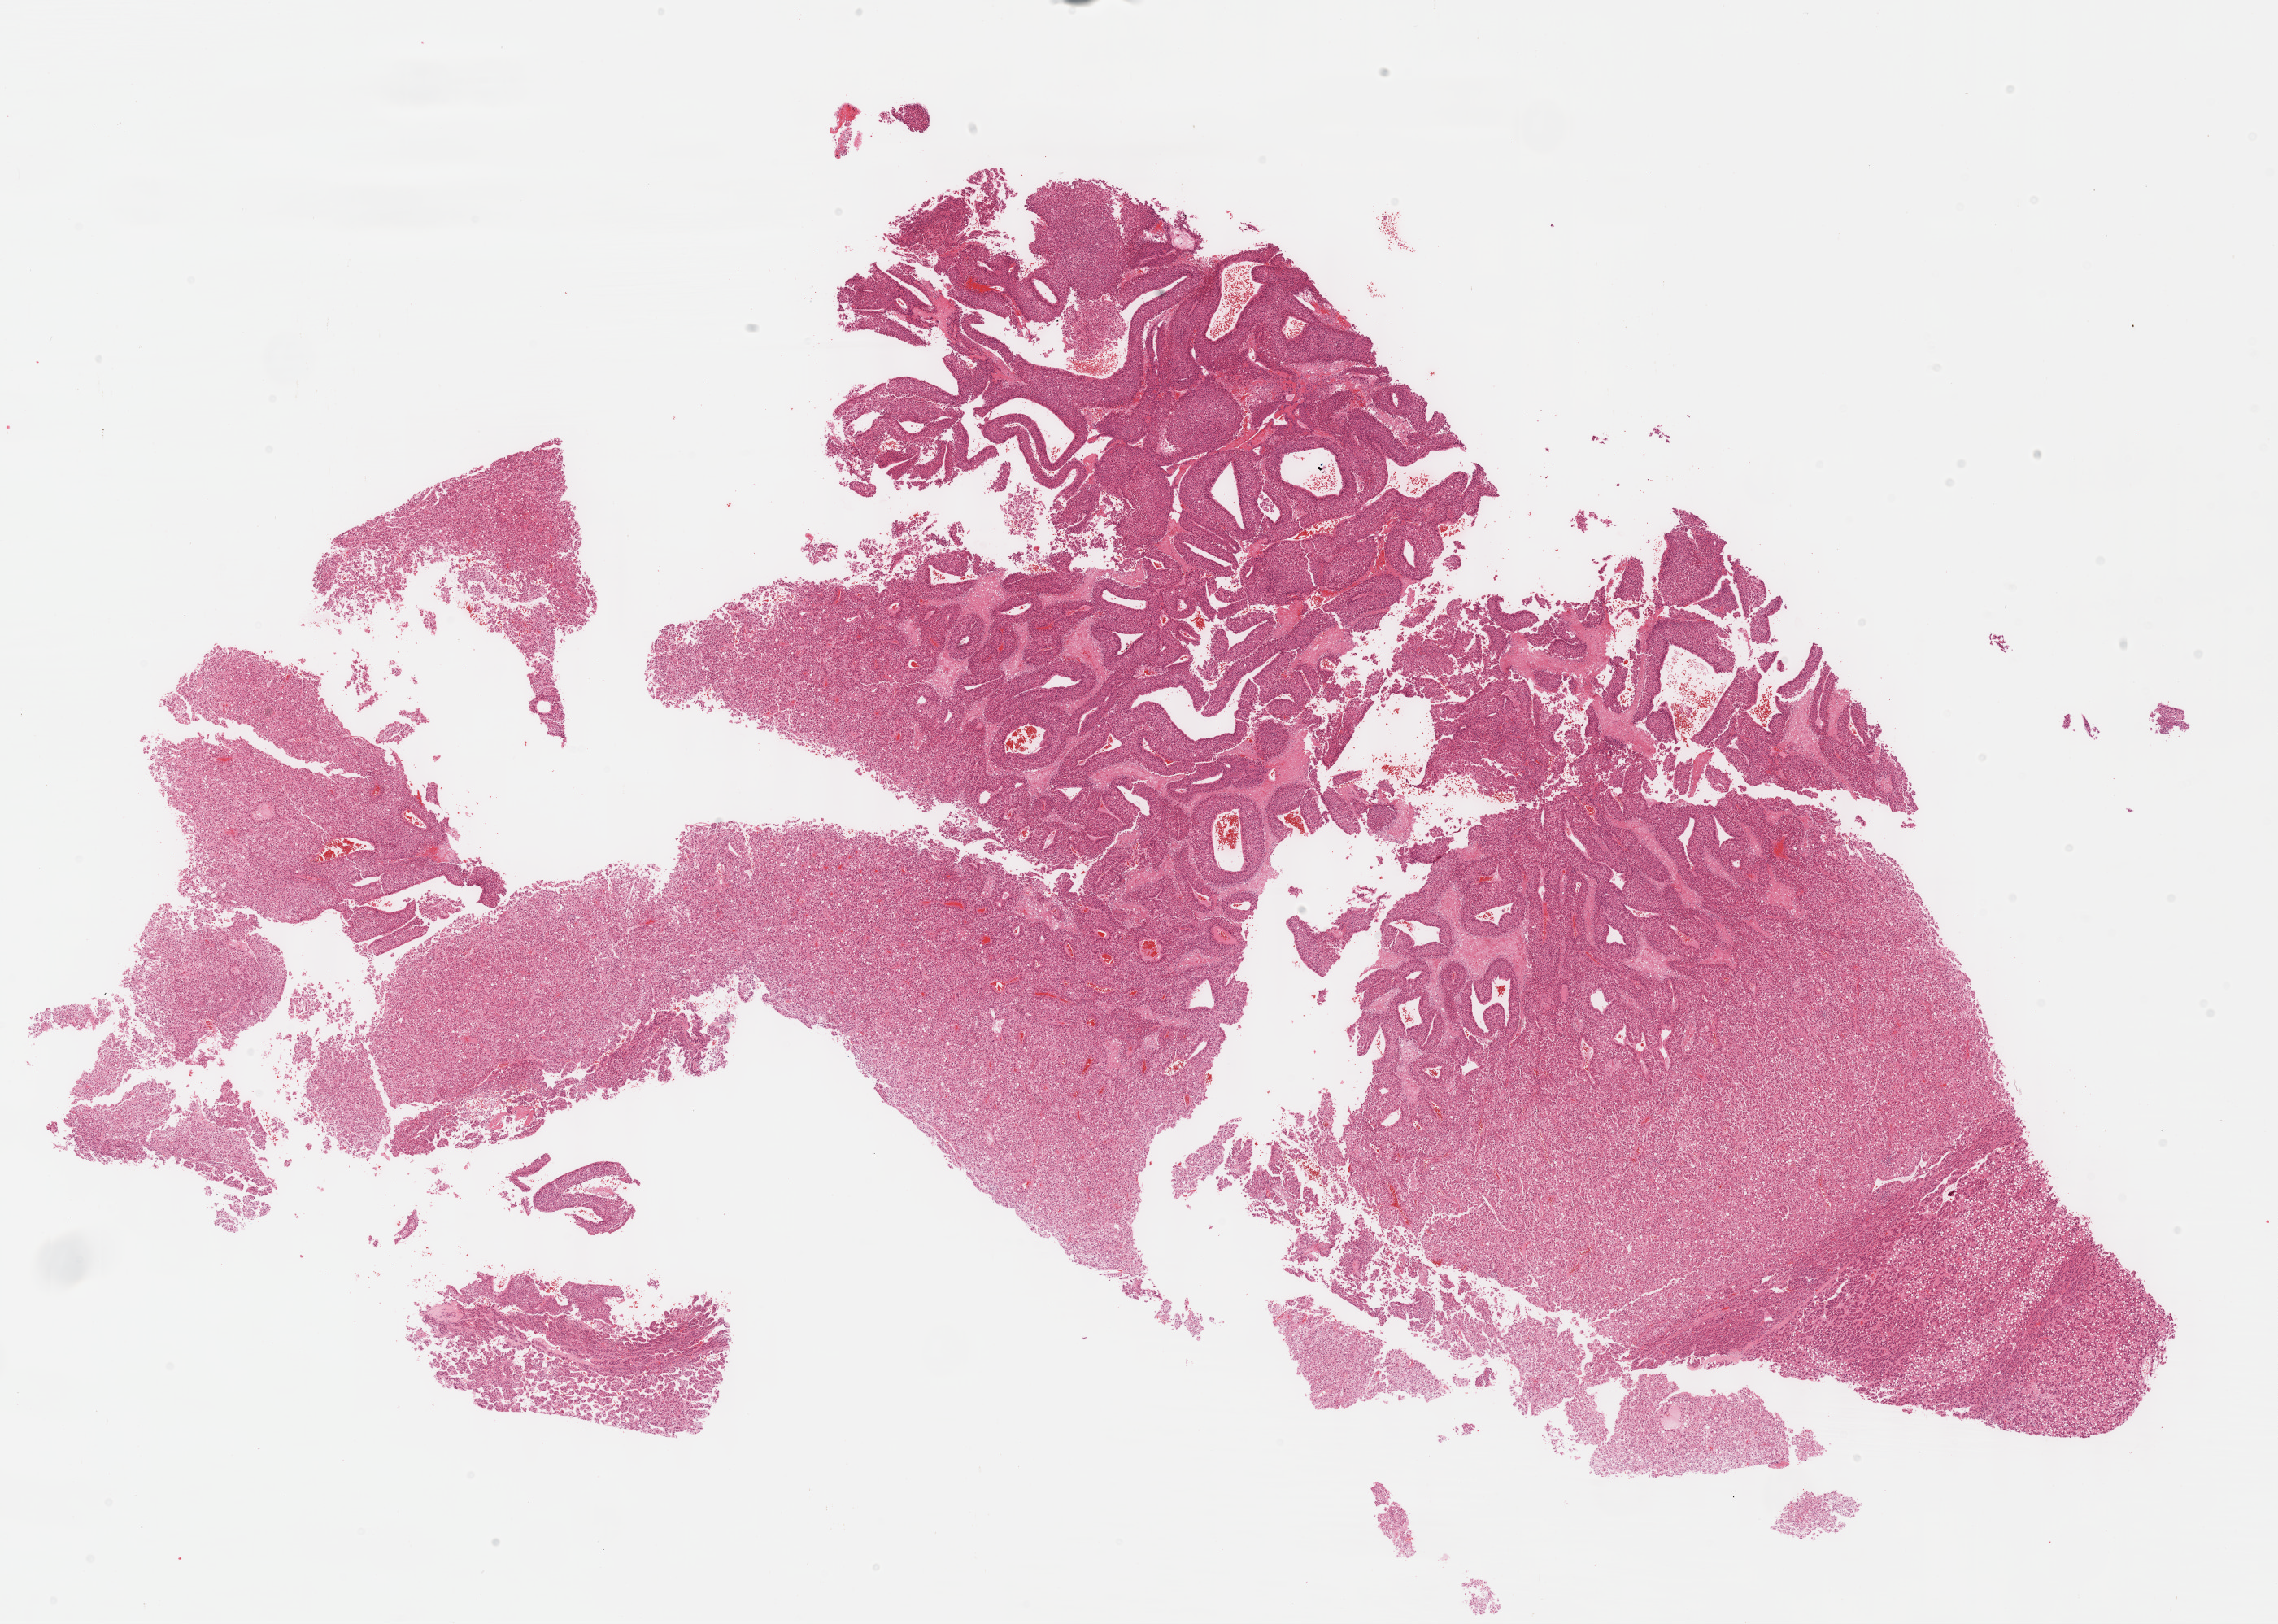
Whole-slide histology image, Hematoxylin and eosin (H&E) stained, shown as a low-resolution overview of the whole scanned area (about 22.6 x 16.1 mm), formalin-fixed paraffin-embedded (FFPE) diagnostic section, primary tumour sample from the liver. Female, age 73 years at initial diagnosis. Histologic grade: G2 (moderately differentiated).
Histologic diagnosis: Hepatocellular carcinoma, NOS. AJCC pathologic stage: I.